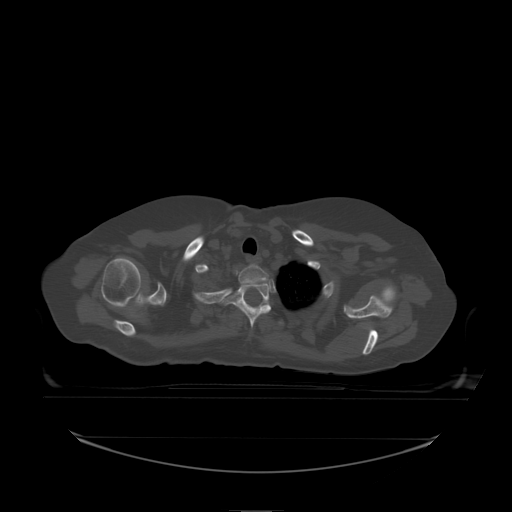
CT including the spine, one axial slice; slice 181 of 242 in the series (ordered by position); bone window (W 1800 / L 400 HU); 512 × 512 image matrix, field of view 500 × 500 mm. Patient: female, 53 years. From the clinical record (not read from this slice): primary cancer: lung.
Structures marked on this image (semi-automatic segmentation, software-assisted and operator-edited):
- T1 vertebra: bounding box (x1, y1, x2, y2) in pixels: (239, 264, 270, 285)
- T2 vertebra: (220, 283, 271, 328)